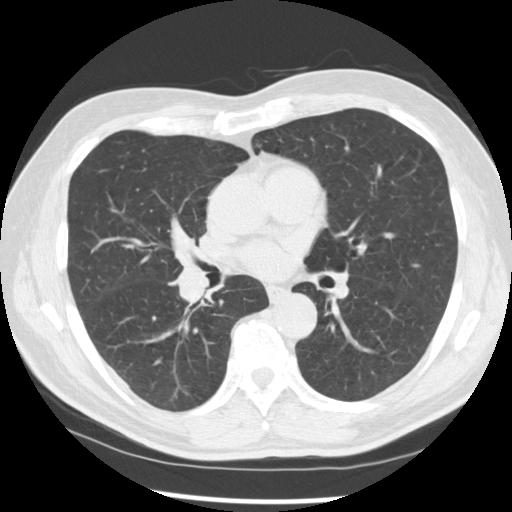
Low-dose screening chest CT, axial slice, baseline annual screen, lung window (W 1500 / L -600 HU), 120 kVp, slice 149 of 277 in the series, 512 × 512 image matrix, field of view 365 × 365 mm. Male, age 67 years at enrolment.
- Lesion marked by an expert reader, bounding box <158,247,228,312> (left, top, right, bottom; pixels).
- The exam's reader record, not a measurement of the box and not confirmed to be the same lesion: non-calcified nodule or mass ≥4 mm, left lower lobe, 15 × 15 mm, spiculated (stellate) margins, soft tissue attenuation.
- Note: the box lies in the patient's right hemithorax on this image, whereas the reader's record names the left lung; they may be different findings.
- Official screen result: positive, change unspecified: nodule(s) >= 4 mm or enlarging nodule(s), mass(es), or other non-specific abnormalities suspicious for lung cancer.
- Later outcome: lung cancer diagnosed 49 days after this screen — squamous cell carcinoma, NOS, right middle lobe, poorly differentiated (G3), stage IIB (AJCC 6th edition), 35 mm at pathology.